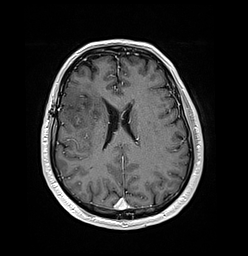
Brain MRI from a brain-tumour surgery series, one axial slice; position 64 of 176 along the scan axis; T1-weighted post-contrast; 248 × 256 image matrix, field of view 242 × 250 mm. From the clinical record (not read from this slice): histopathology: Oligodendroglioma; WHO grade: 3; IDH mutation: yes; tumour location: Right Frontal.
Annotated regions visible in this slice (manually delineated by an expert):
- tumour: bounding box [x1, y1, x2, y2] px = [74, 116, 82, 125]